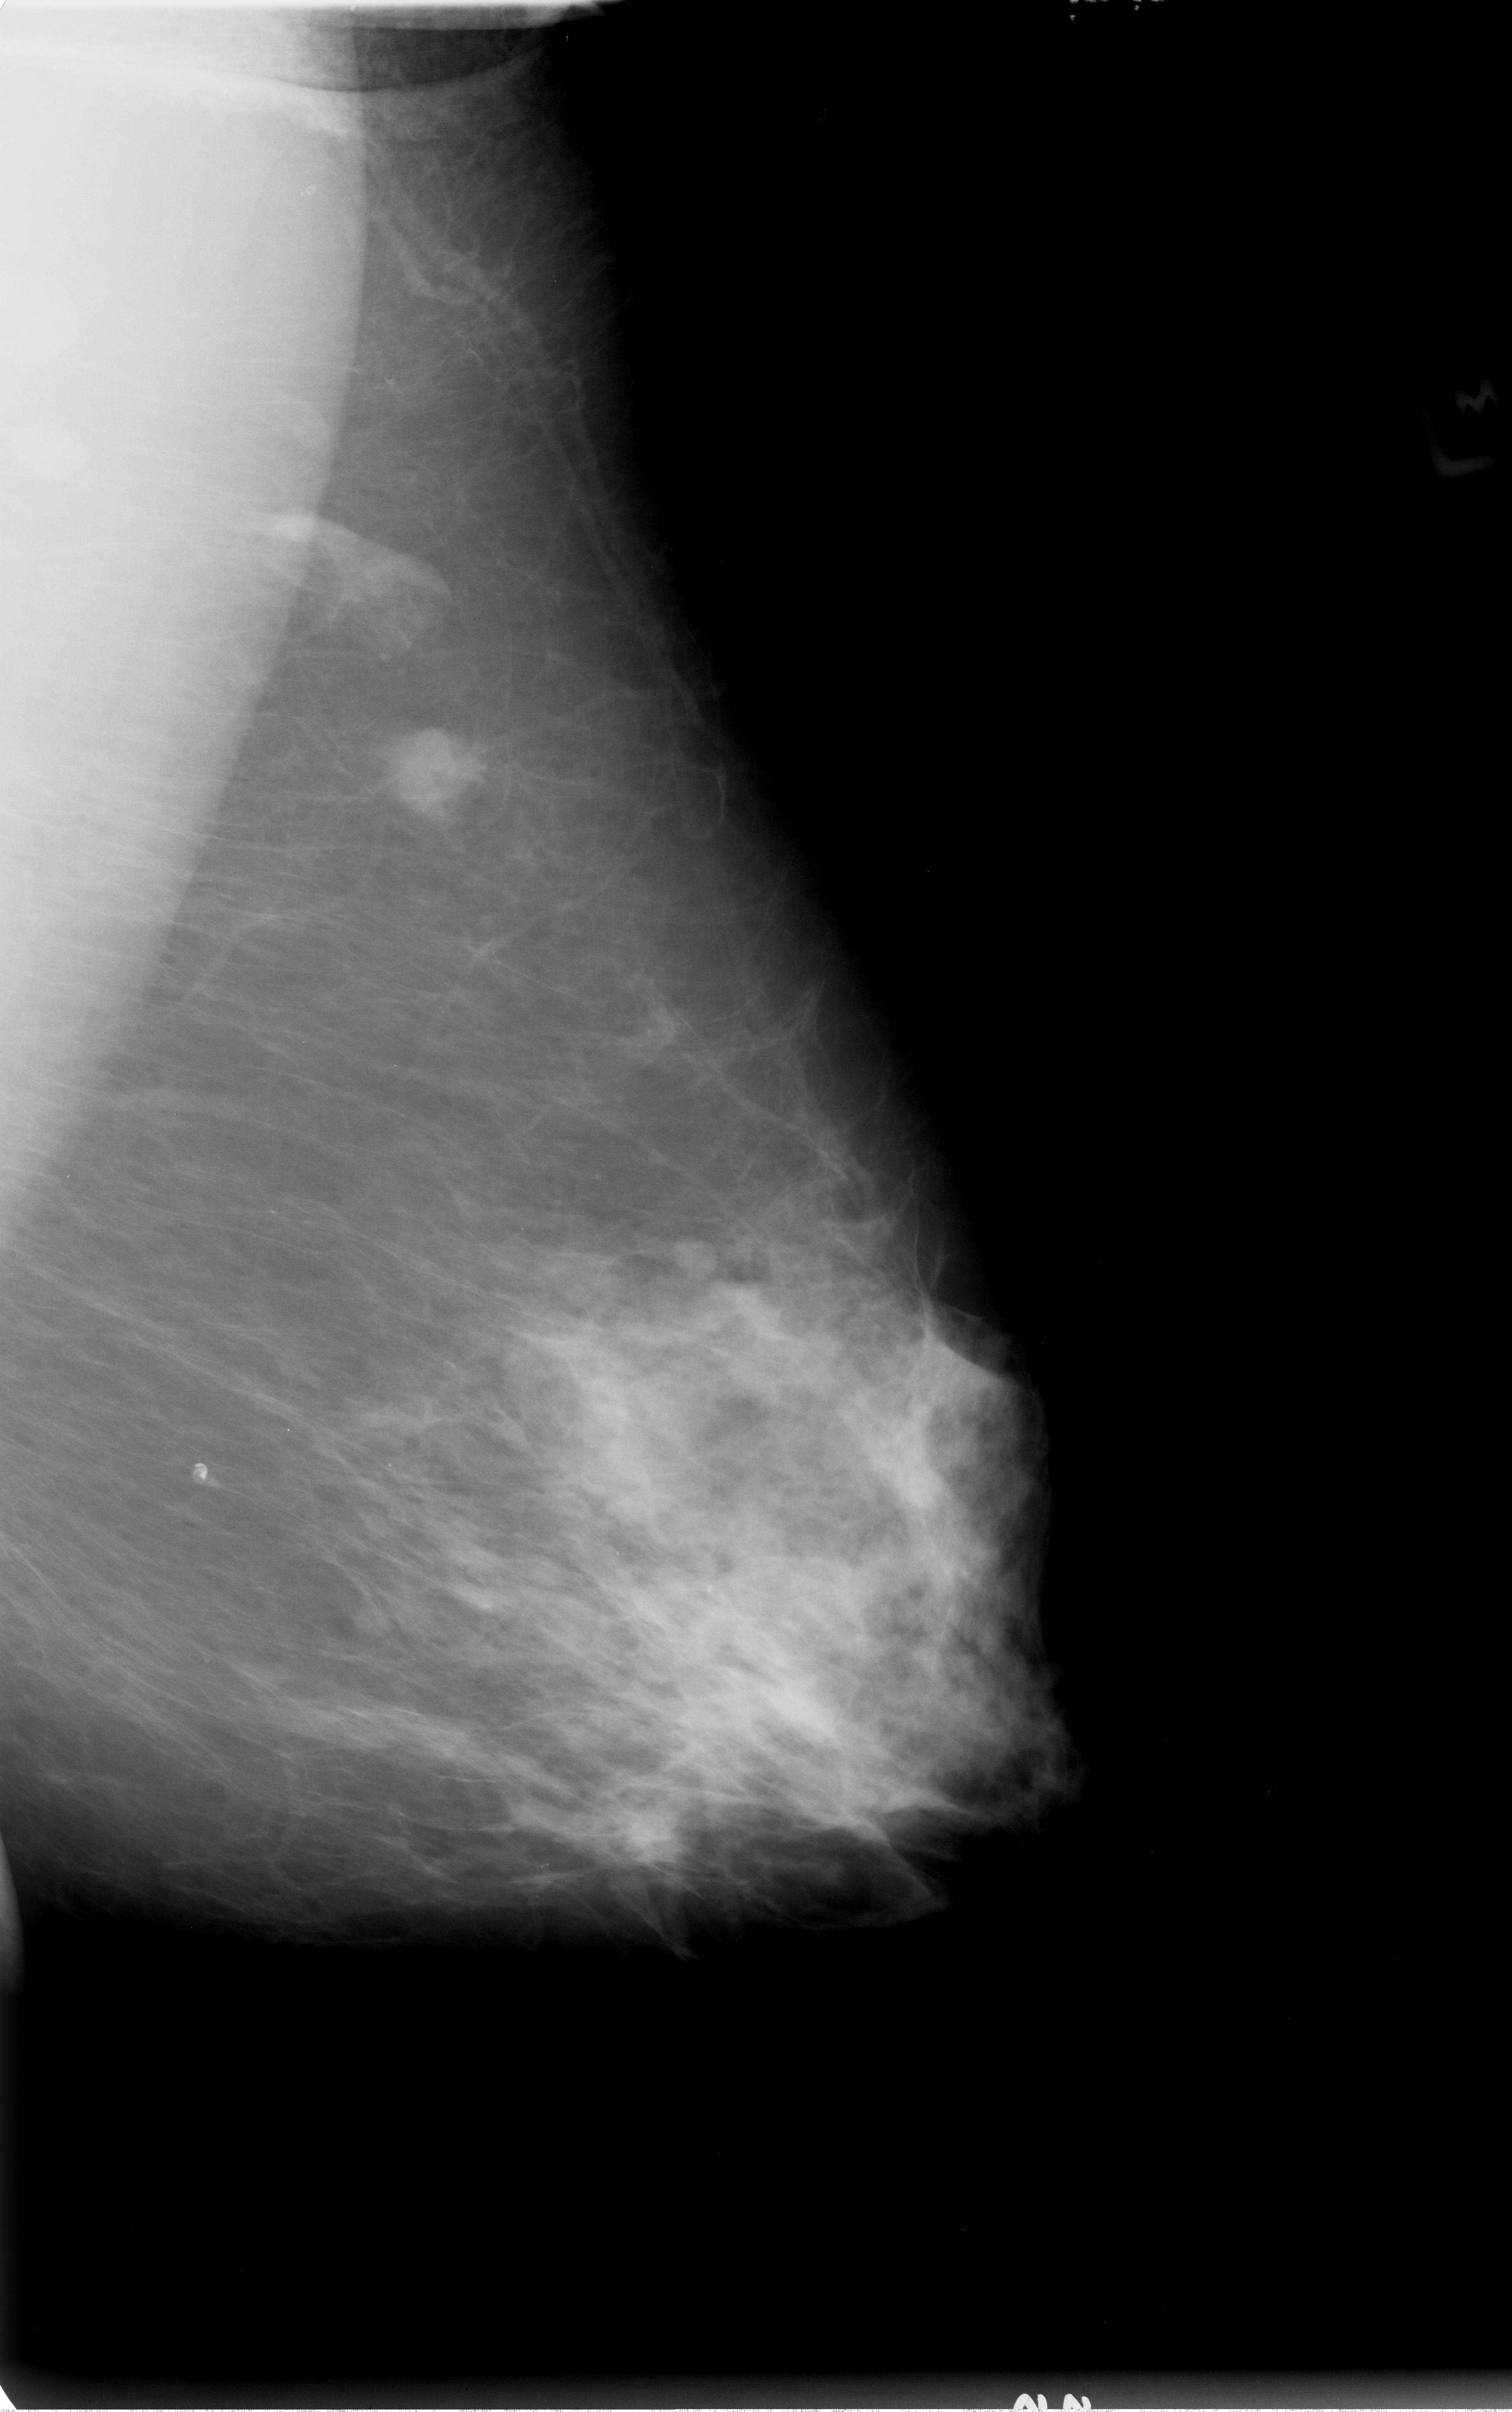
Mammogram (digitized film), left breast, MLO view.
Finding: mass, shape lobulated / irregular, margins ill defined; BI-RADS assessment category 4; subtlety rating 4 on a 1 (subtle) to 5 (obvious) scale; pathology (as recorded): malignant.